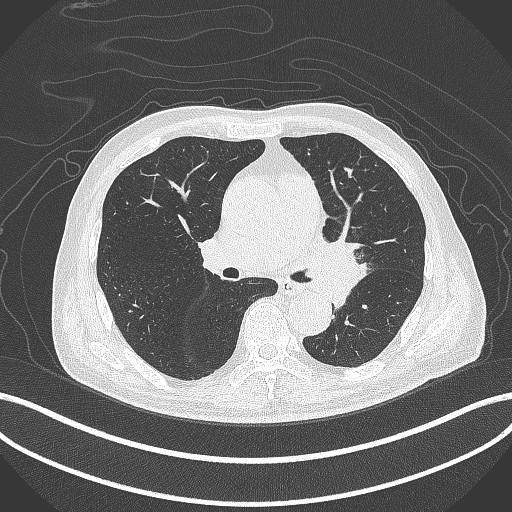
Chest CT, one axial slice; slice 248 of 417 in the series (ordered by position); 120 kVp; lung window (W 1500 / L -600 HU); 1 mm slice thickness; 512 × 512 image matrix, field of view 400 × 400 mm. Patient: male, 77 years. From the clinical record (not read from this slice): clinical TNM (as recorded): T3 N1 M0.
Annotated regions visible in this slice (bounding box drawn by a radiologist):
- lung tumour (recorded histology: adenocarcinoma): bounding box (x1, y1, x2, y2) in pixels: (301, 236, 364, 304)